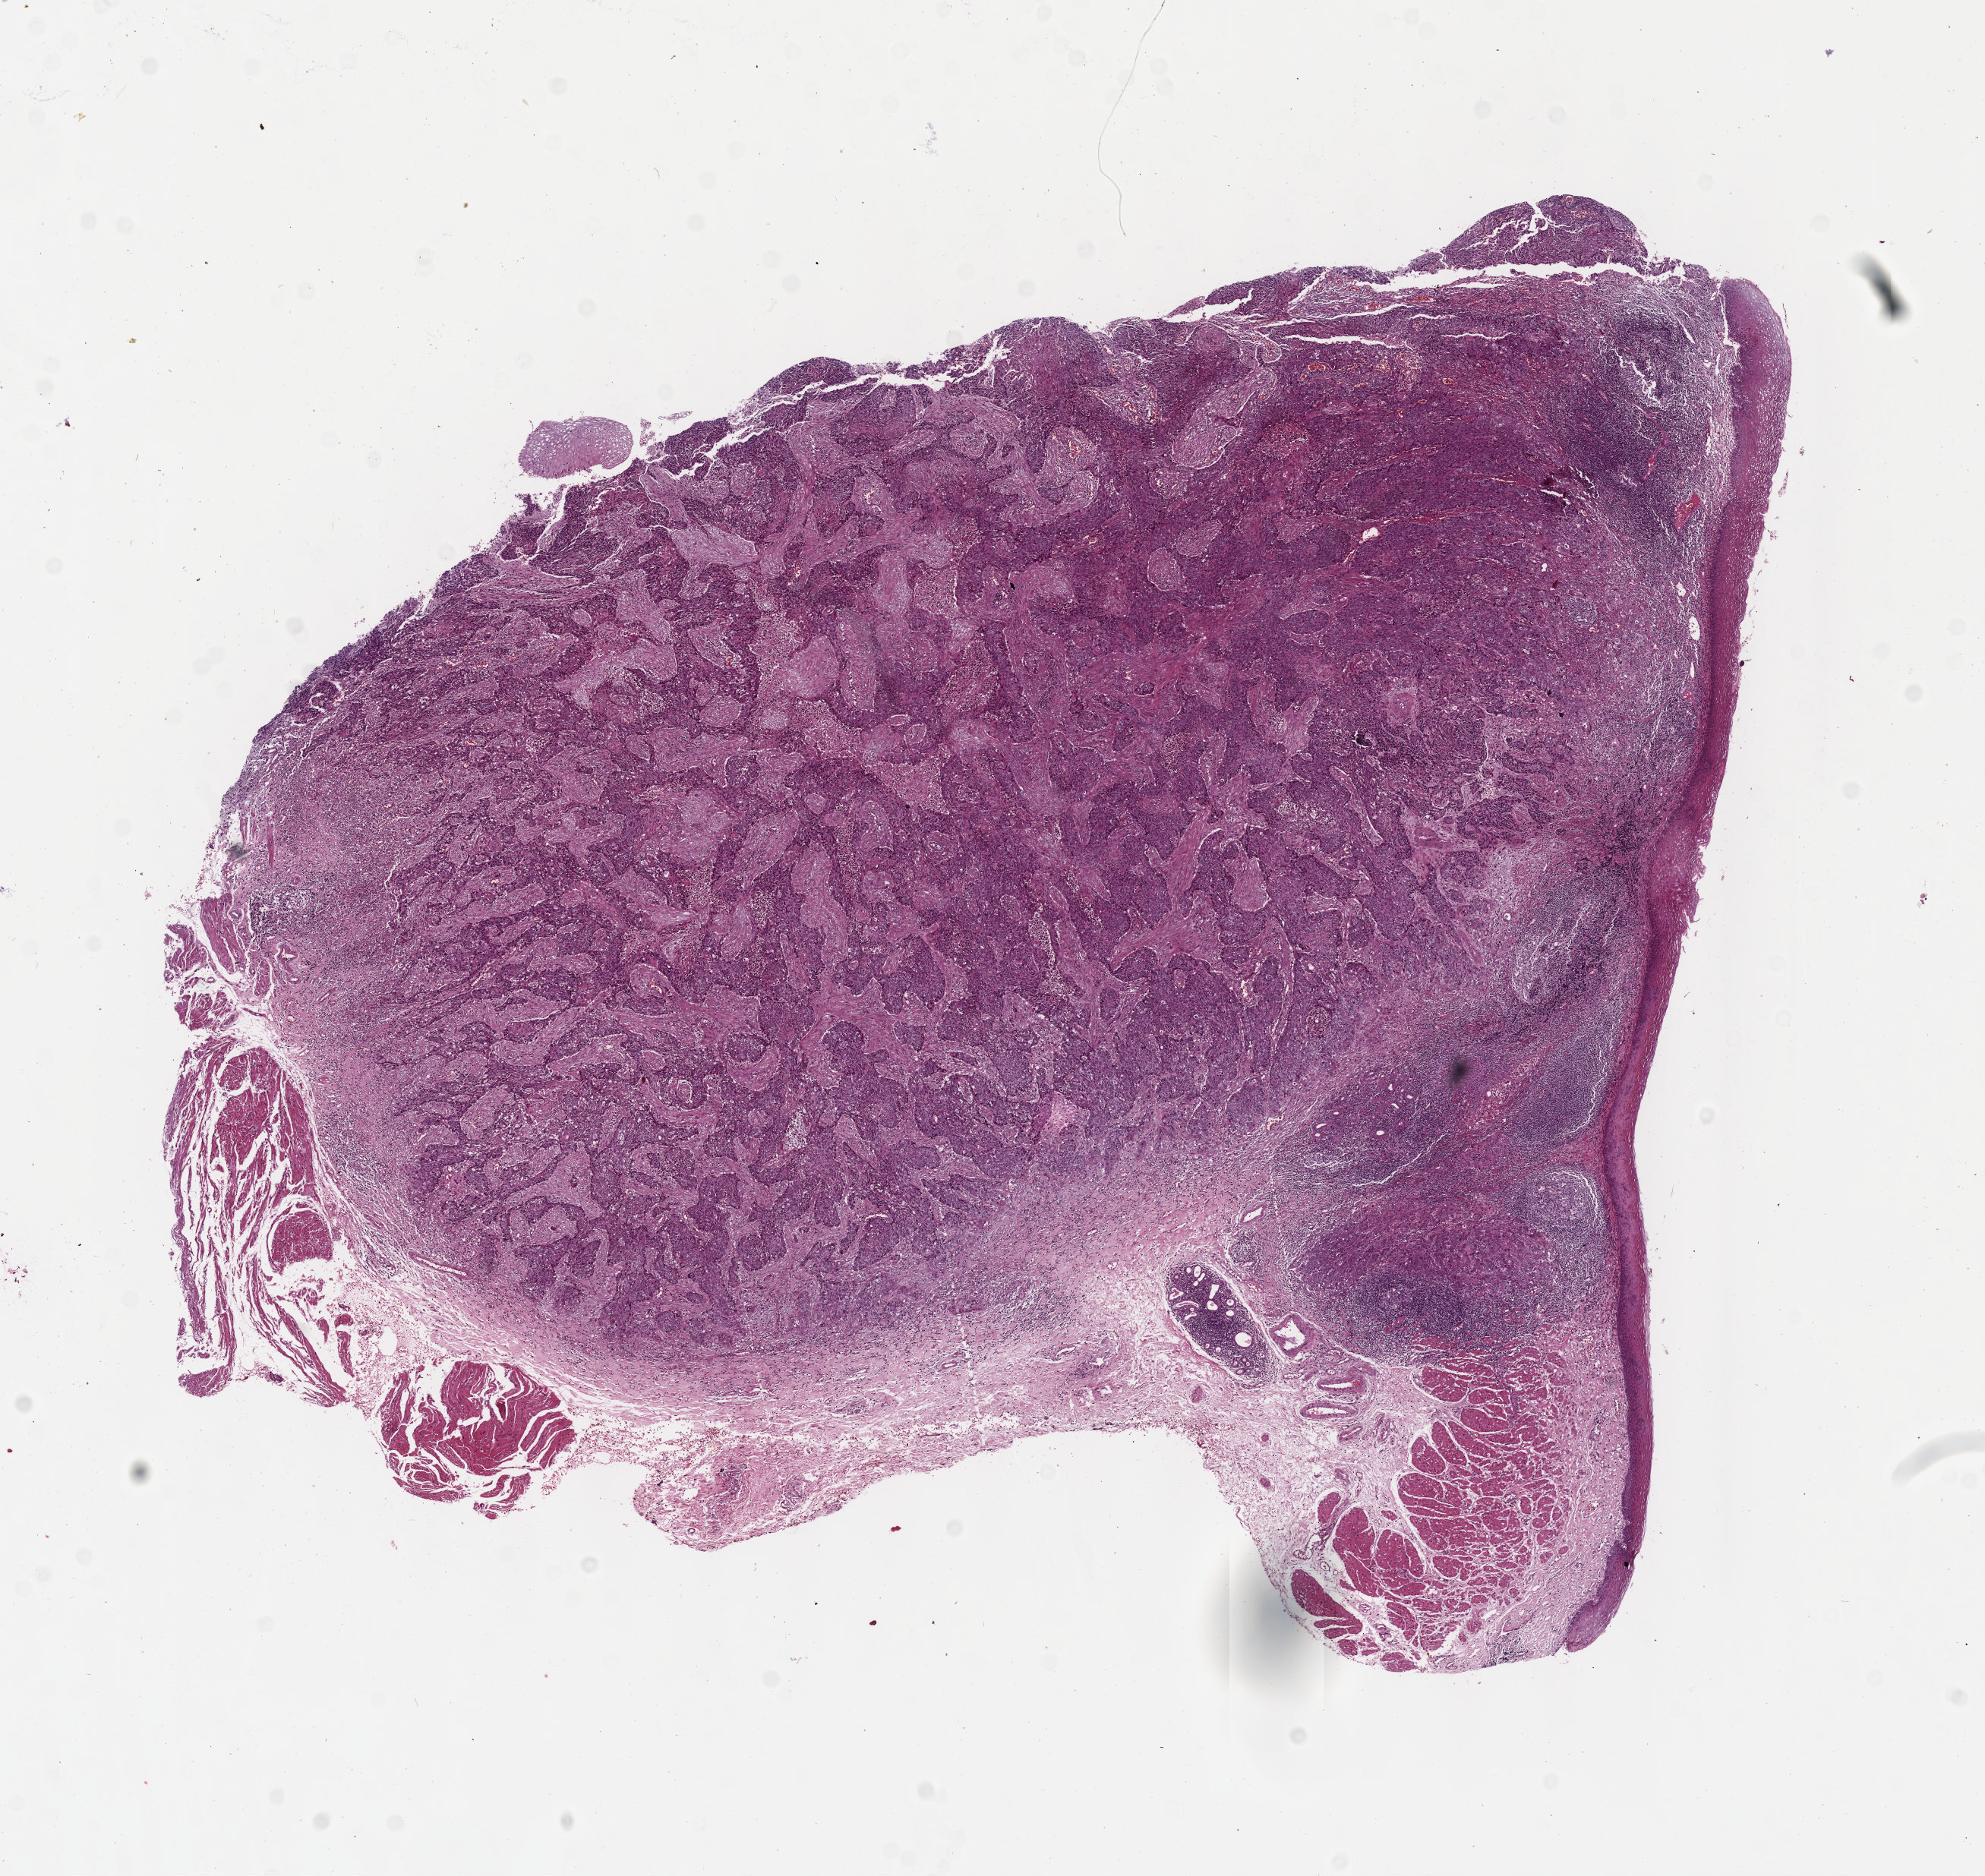
H&E-stained whole-slide image — low-resolution overview of the scanned area, about 10.6 x 10.0 mm; formalin-fixed paraffin-embedded (FFPE) diagnostic section; esophagus, primary tumour sample. Female, age 60 years at initial diagnosis. Histologic grade: G3 (poorly differentiated).
AJCC pathologic stage: IIA. TNM: T2 N0 M0. Histologic diagnosis: Squamous cell carcinoma, NOS.